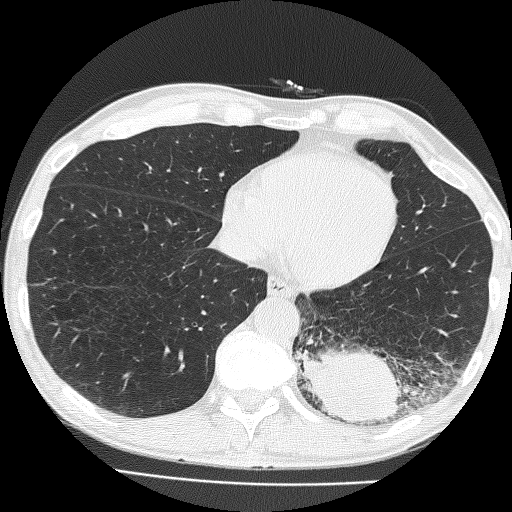
Low-dose screening chest CT, one axial slice. Slice 53 of 160 in the series (ordered by position). Reconstruction kernel FC51. Lung window (W 1500 / L -600 HU). 2 mm slice thickness. 512 × 512 image matrix, field of view 324 × 324 mm.
Structures marked on this image (manually delineated by an expert):
- lesion 1 (tumor, lower lobe of left lung): box from (x=296, y=347) to (x=407, y=426) px